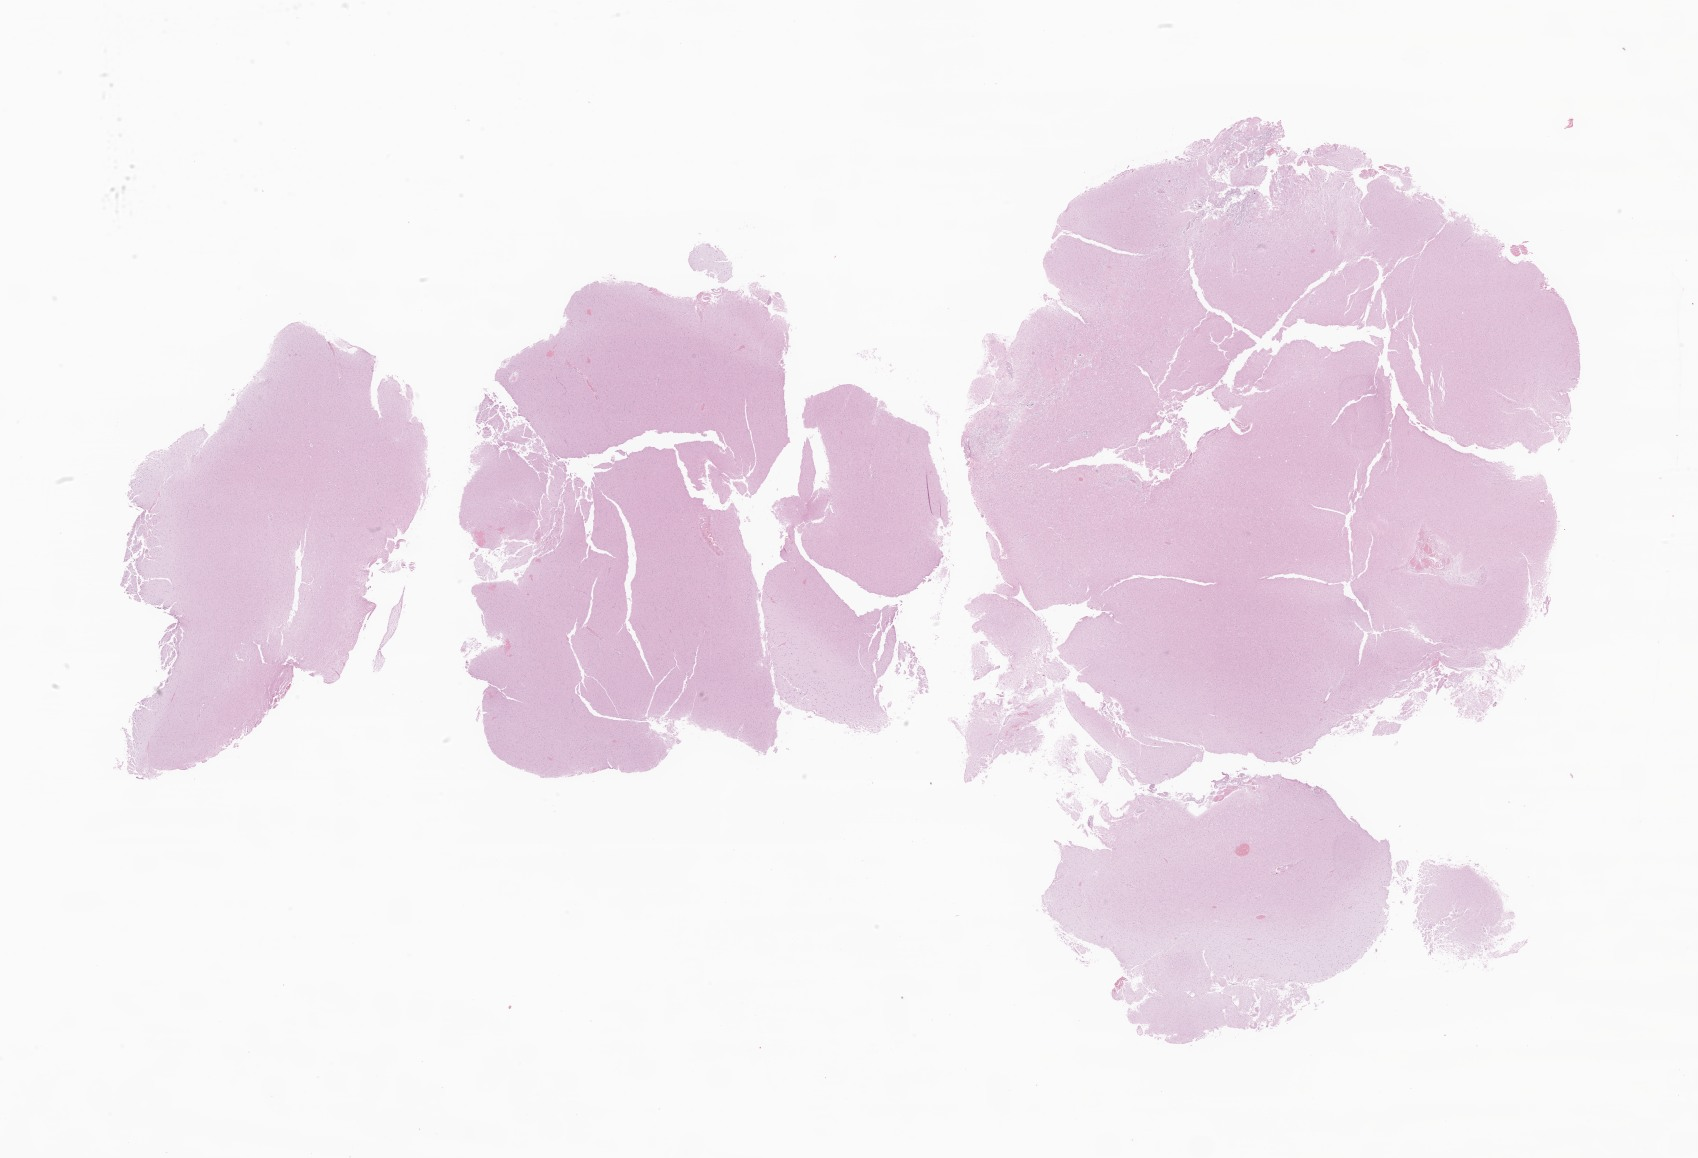
Whole-slide image, hematoxylin and eosin (H&E) stain of tumor tissue from the brain, whole scanned area (about 28.6 x 19.5 mm) shown as a low-resolution overview; formalin-fixed paraffin-embedded section. Female patient, age 50 months.
- diagnosis: Glioma, malignant